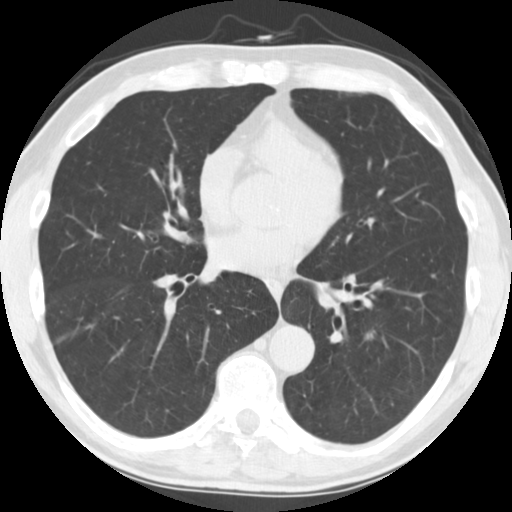
Axial slice from a low-dose chest CT screening exam; second screening round (one year after baseline); lung window (W 1500 / L -600 HU); 2.5 mm slice thickness. Male participant, aged 64 years at enrolment. Current smoker at enrolment.
- Expert reader's lesion annotation, bounding box (x1, y1, x2, y2) in pixels: (357, 321, 386, 349).
- Screening reader's record for this exam: no non-calcified nodule ≥4 mm recorded.
- Official screen result: negative screen, no significant abnormalities.
- Participant outcome: lung cancer diagnosed 561 days after this screen — adenocarcinoma, NOS, left lower lobe, stage IV (AJCC 6th edition), 44 mm at pathology.